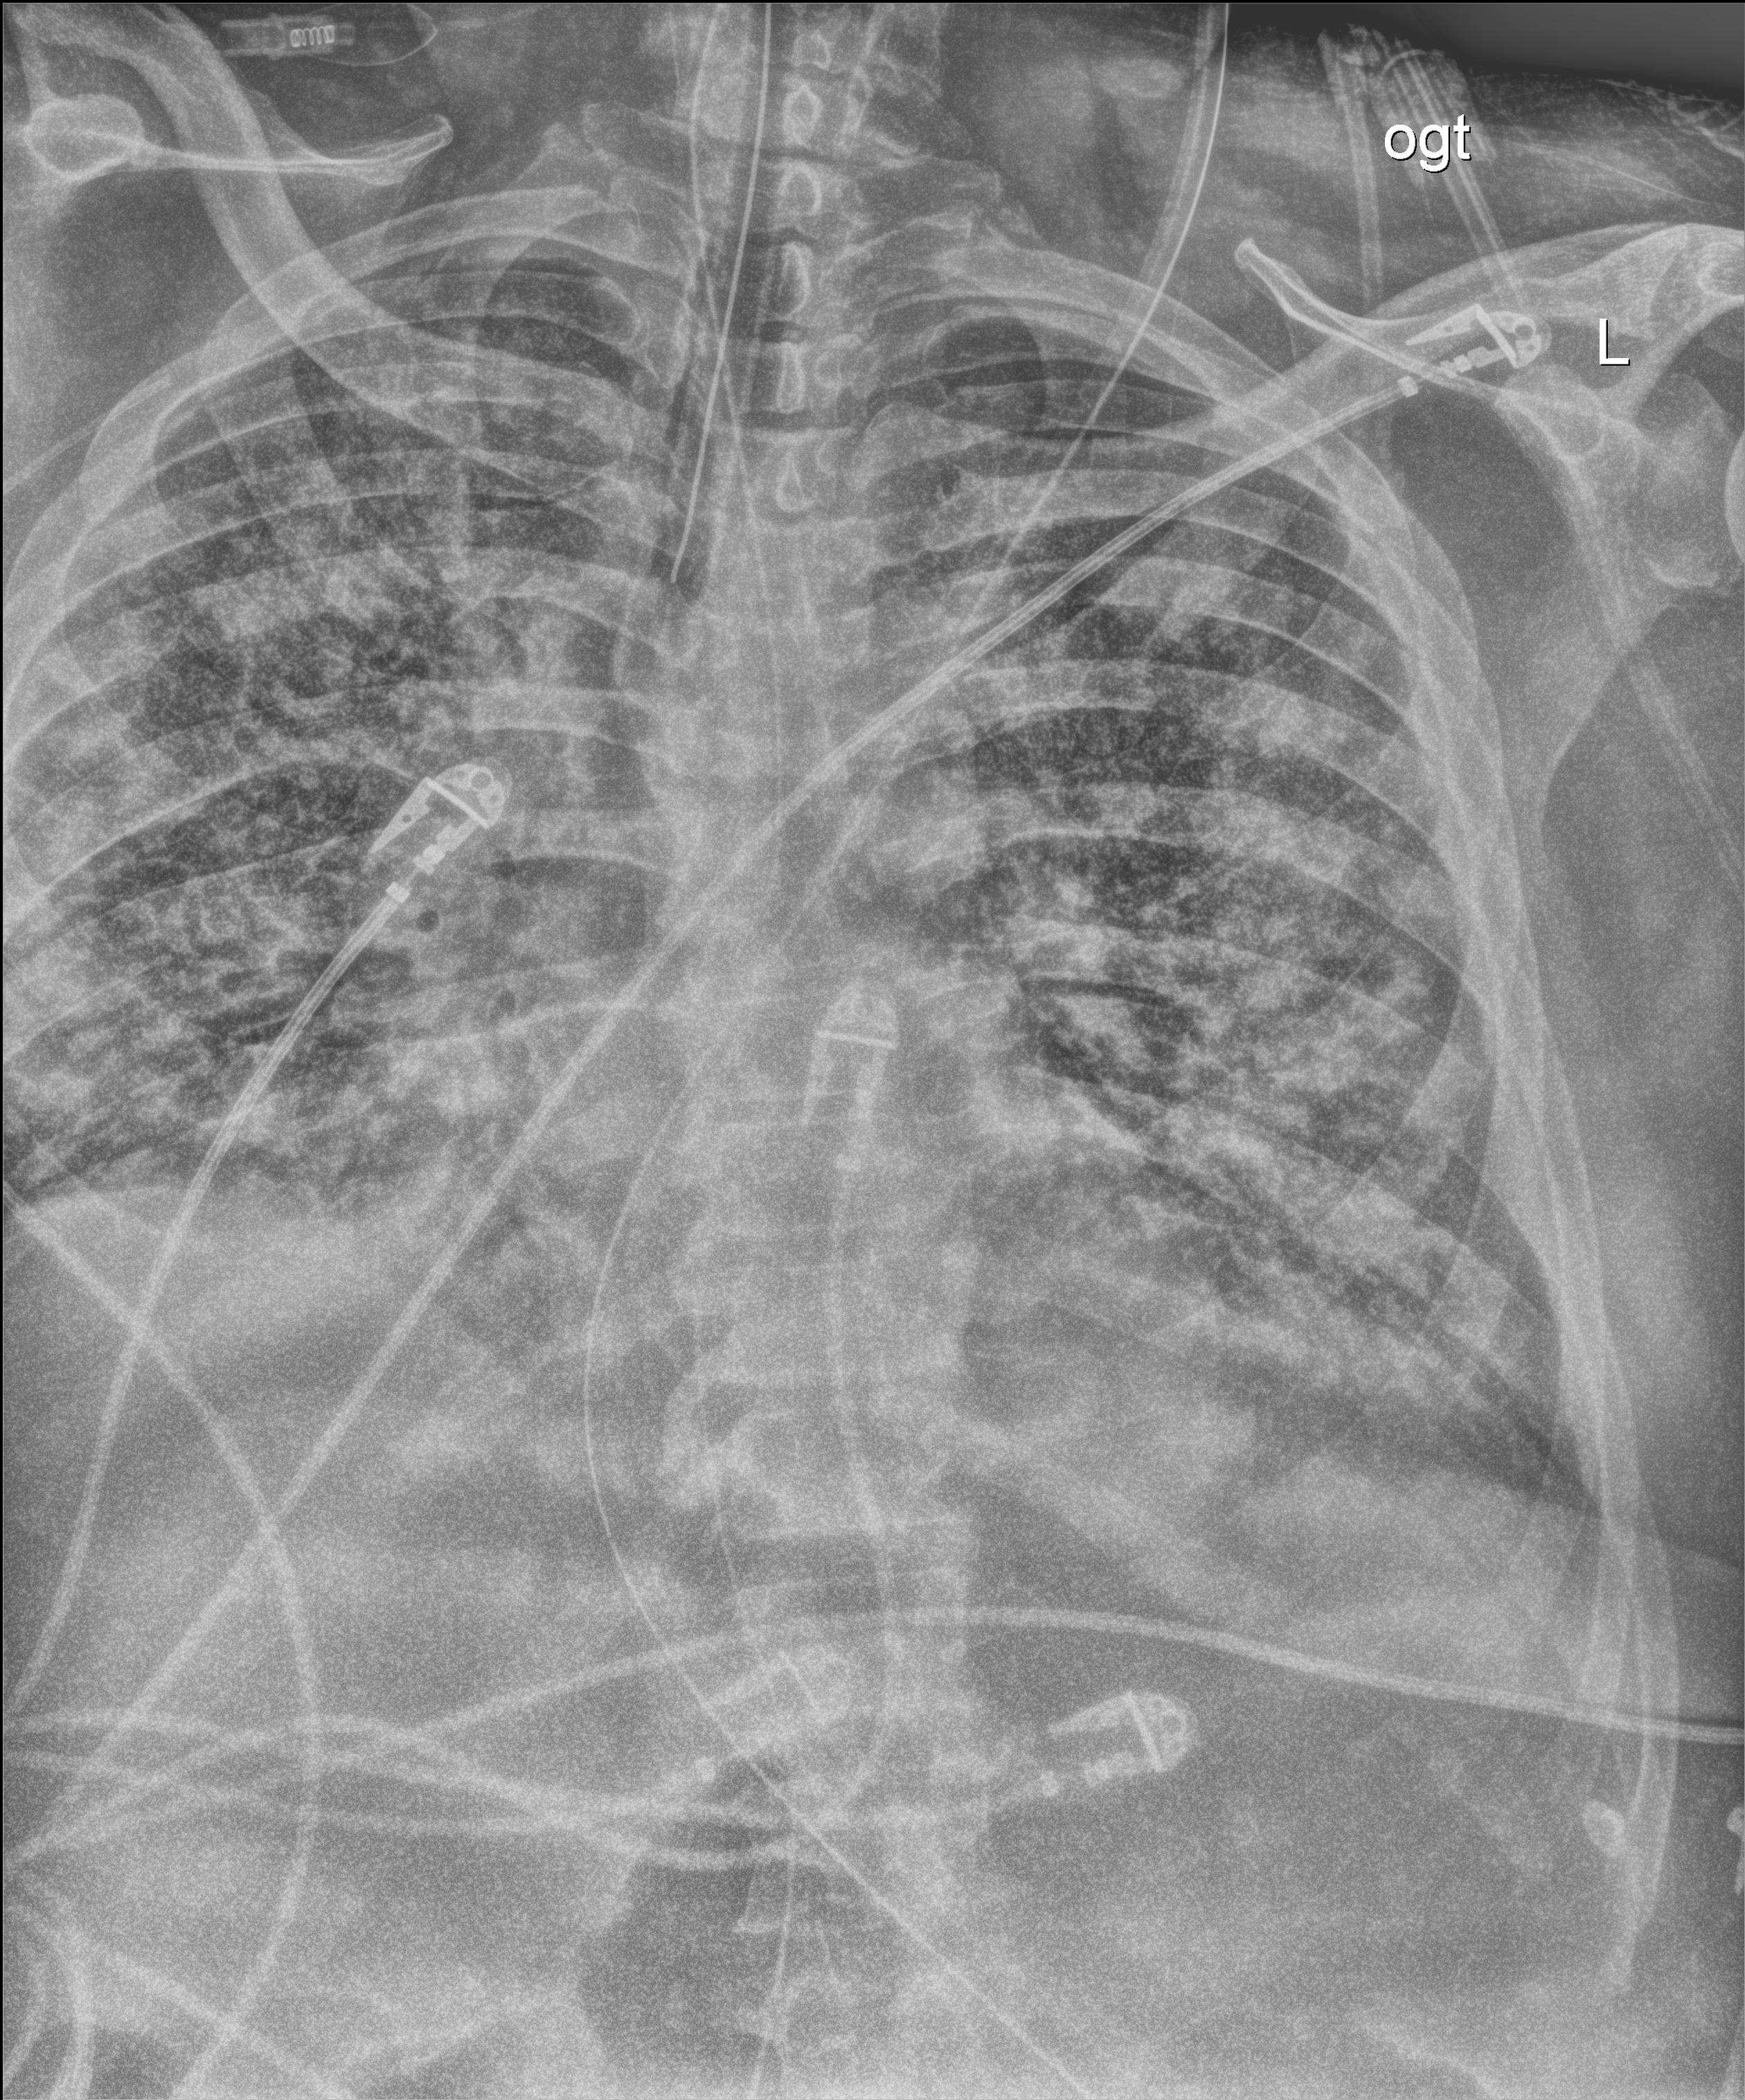
Bedside chest radiograph (digital radiography). Male patient hospitalised with COVID-19, age 60–74 years.
From the hospital-stay record, not from the radiograph (when in the stay this image was taken is not recorded): admitted to intensive care during this hospital stay: yes.